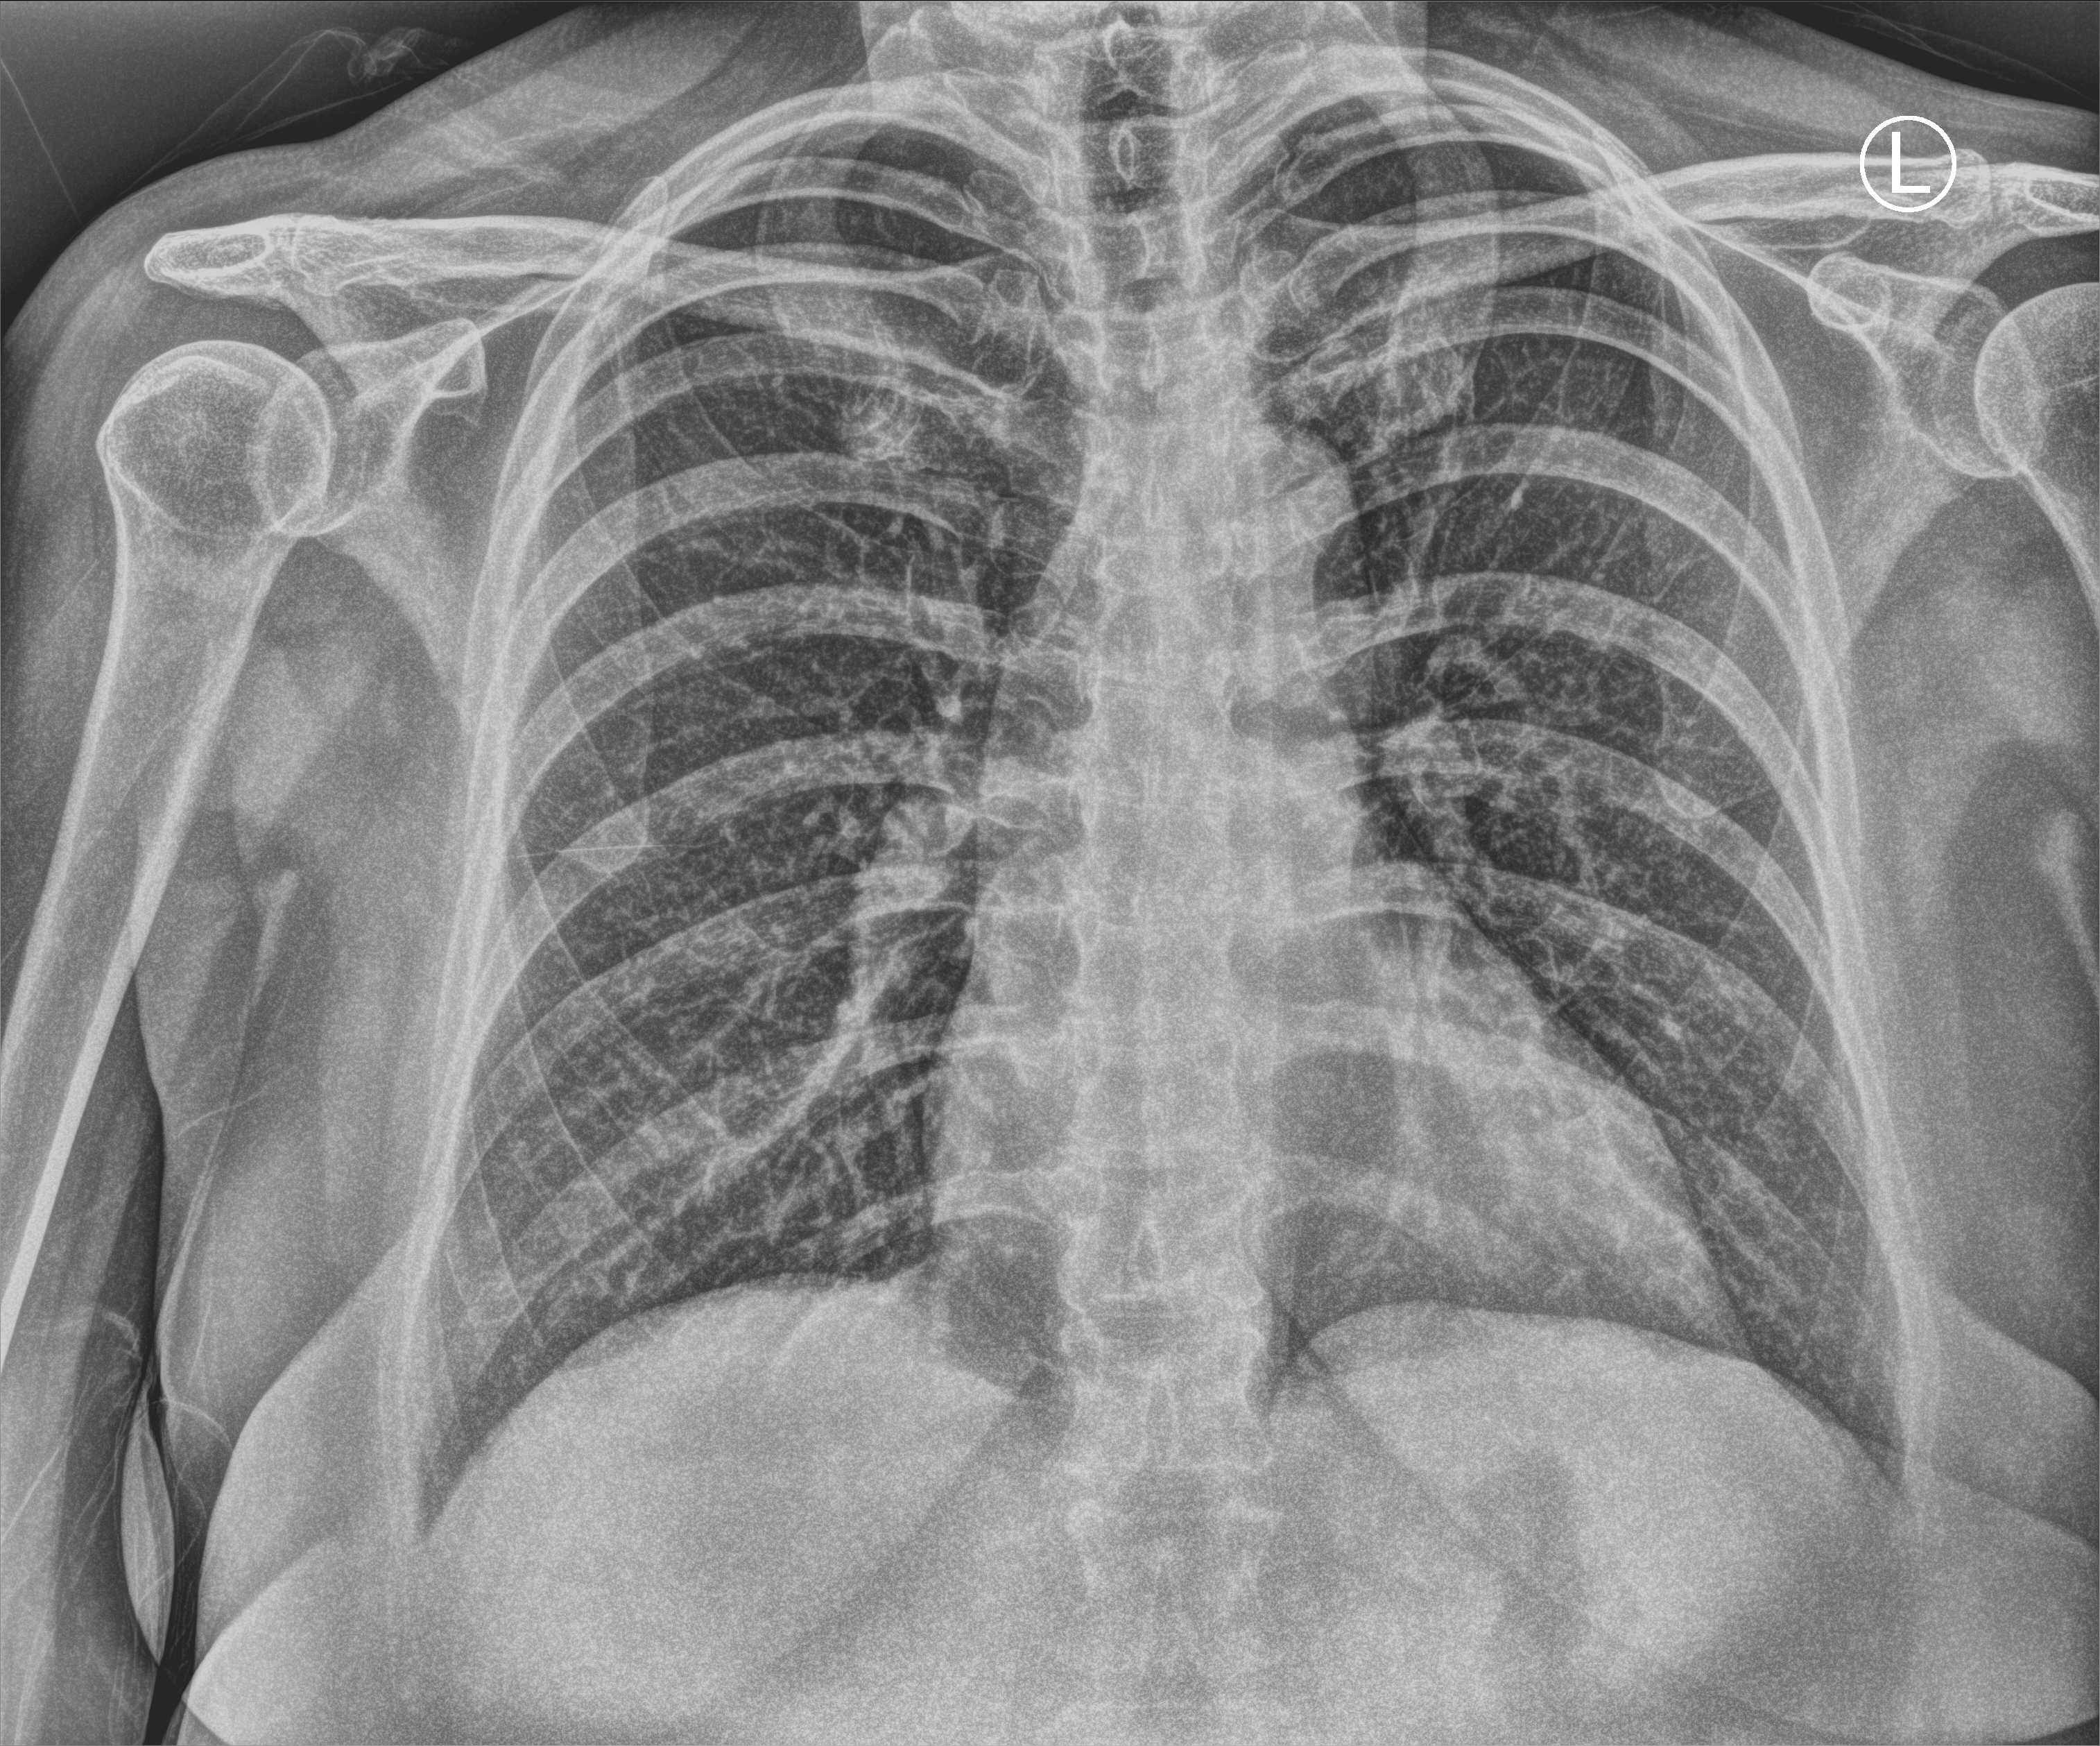
Chest X-ray (portable); anteroposterior (AP) projection. Patient hospitalised with COVID-19; female, aged 18–59 years.
Hospital-stay facts (about this admission, not read from this image; timing relative to this image not recorded): mechanically ventilated during this hospital stay: yes.